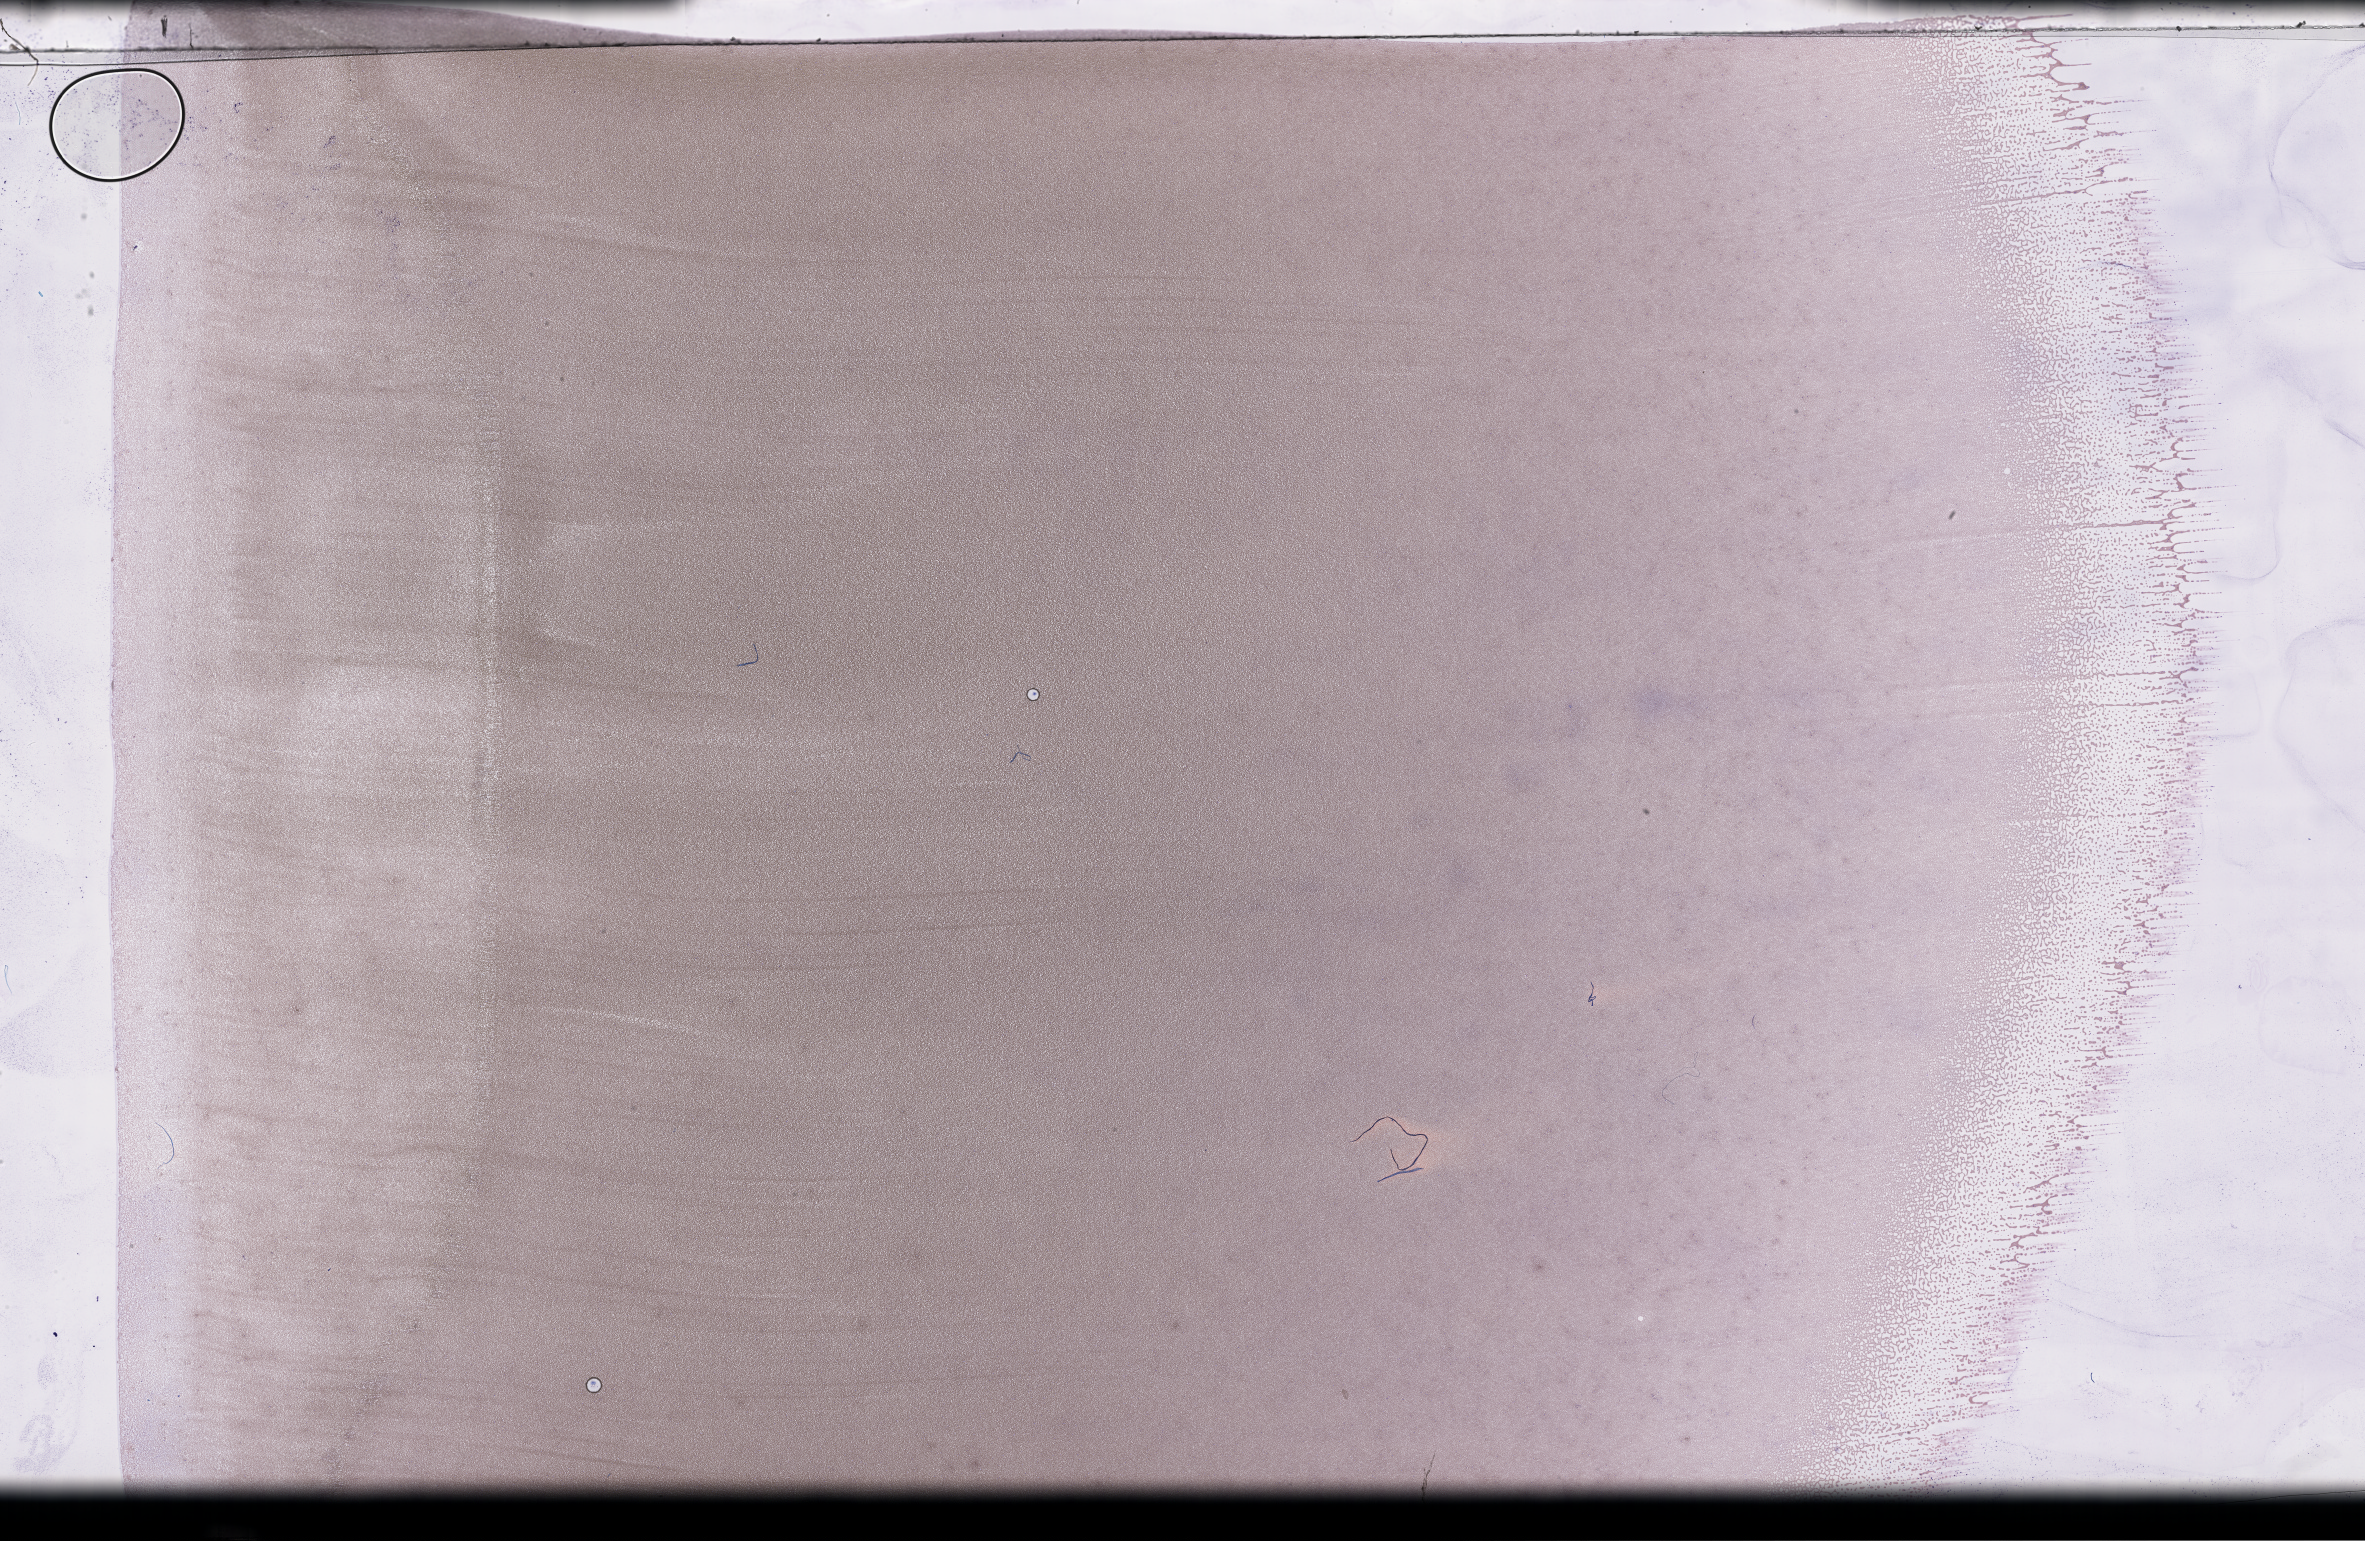
Wright–Giemsa-stained whole blood smear, whole-slide image — whole scanned area (about 38.2 x 24.9 mm) shown as a low-resolution overview. Collected on treatment. Patient sex: female.
Patient diagnosis: Plasma Cell Myeloma.